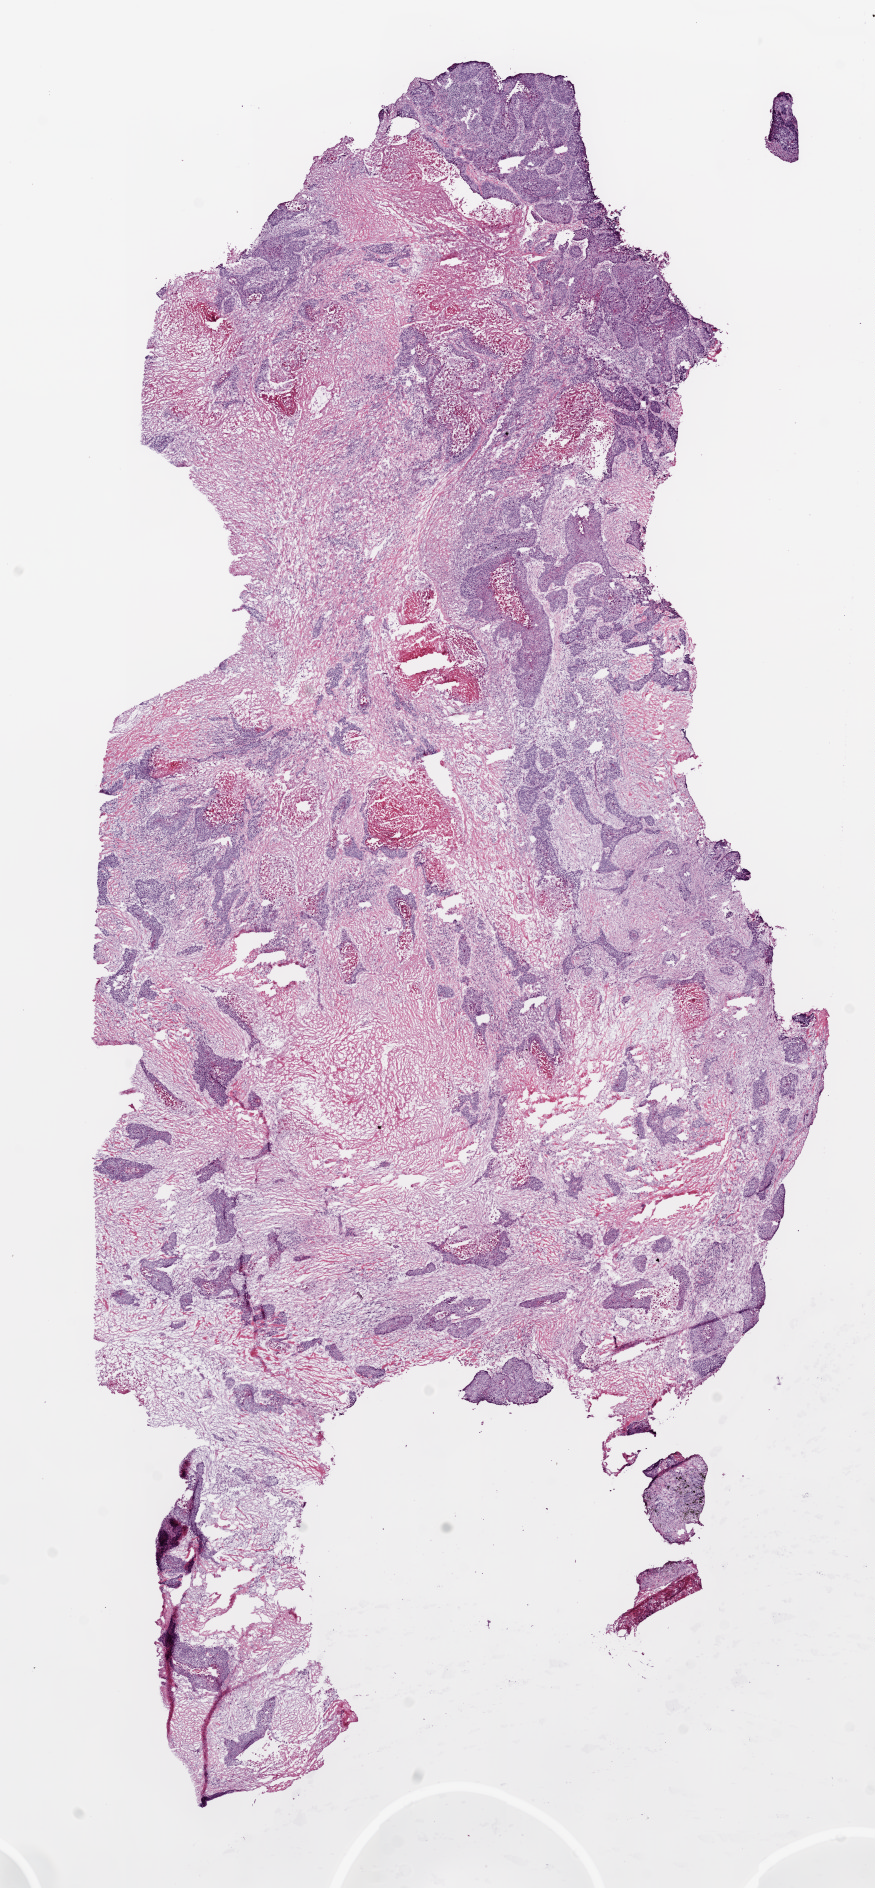
Hematoxylin and eosin (H&E) stained whole-slide image, shown as a low-resolution overview of the whole scanned area (about 7.0 x 15.1 mm, from a 20x scan); frozen section; sample: primary tumour, lung. Patient: male, age at initial diagnosis 73 years. Slide review estimates, as recorded: tumour cells 45%, tumour nuclei 60%, normal cells 0%, stromal cells 40%, necrosis 15%.
Laterality: left. AJCC pathologic stage: IIA. Pathologic diagnosis: Squamous cell carcinoma, NOS (upper lobe, lung).